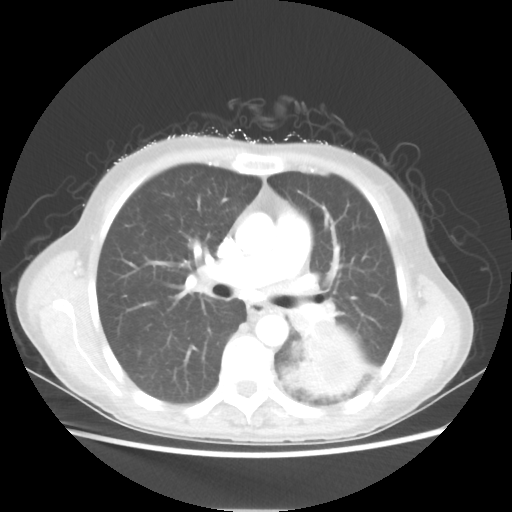
Chest CT, one axial slice; slice 33 of 56 in the series (ordered by position); reconstruction kernel STANDARD; 80 kVp; lung window (W 1500 / L -600 HU); 512 × 512 image matrix, field of view 360 × 360 mm. Patient: female, 53 years. Case-level facts recorded for this patient, not image findings: clinical TNM (as recorded): T3 N0 M0.
Annotated regions visible in this slice (bounding box drawn by a radiologist):
- lung tumour (recorded histology: adenocarcinoma): bounding box <282,321,371,396> (left, top, right, bottom; pixels)